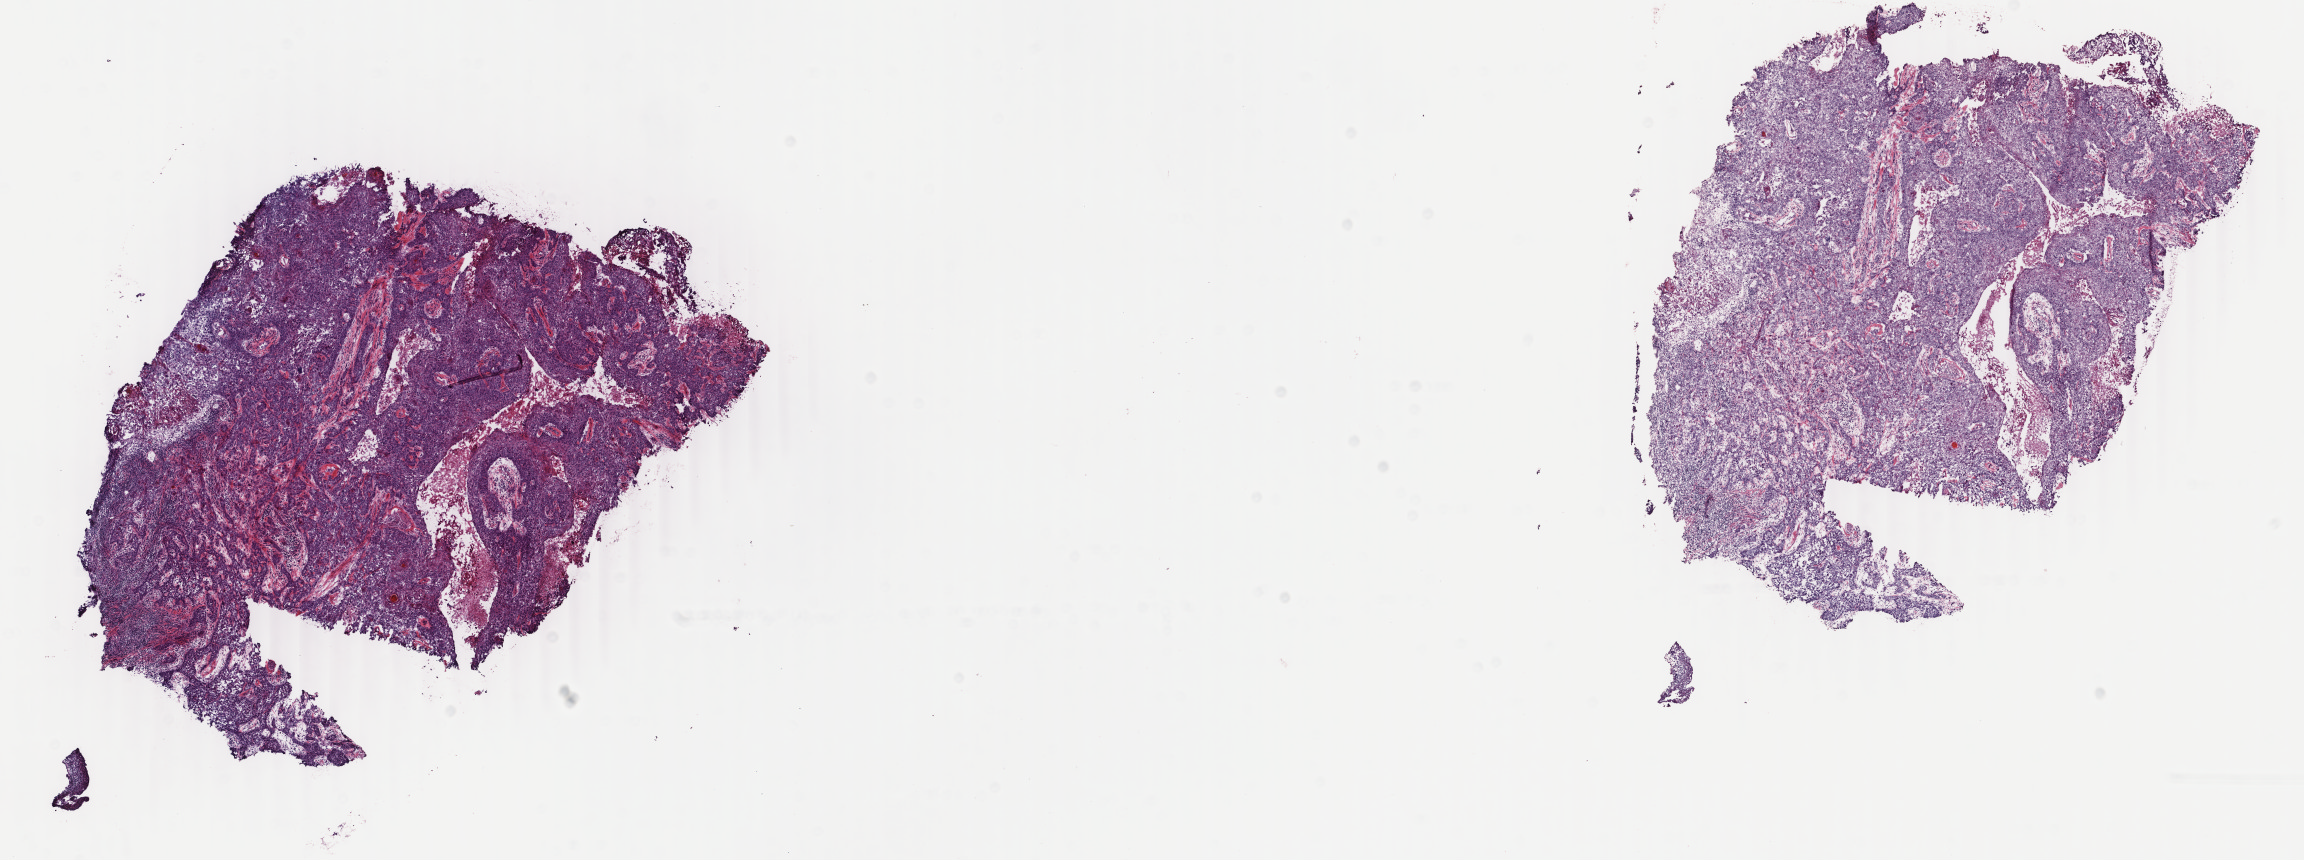
Hematoxylin and eosin (H&E) stained whole-slide image, shown as a low-resolution overview of the whole scanned area (about 18.3 x 6.8 mm). Frozen section from the bottom of the tissue portion. Primary tumour sample from the cervix. Patient: female, age at initial diagnosis 48 years. Histologic grade: G3 (poorly differentiated). Pathologist review of this section (percent, as recorded): tumour cells 85%, tumour nuclei 85%, normal cells 0%, stromal cells 10%, necrosis 5%. Infiltration values recorded for this section: lymphocyte infiltration 7%, monocyte infiltration 0%, neutrophil infiltration 0%.
- diagnosis: Squamous cell carcinoma, NOS (cervix uteri)